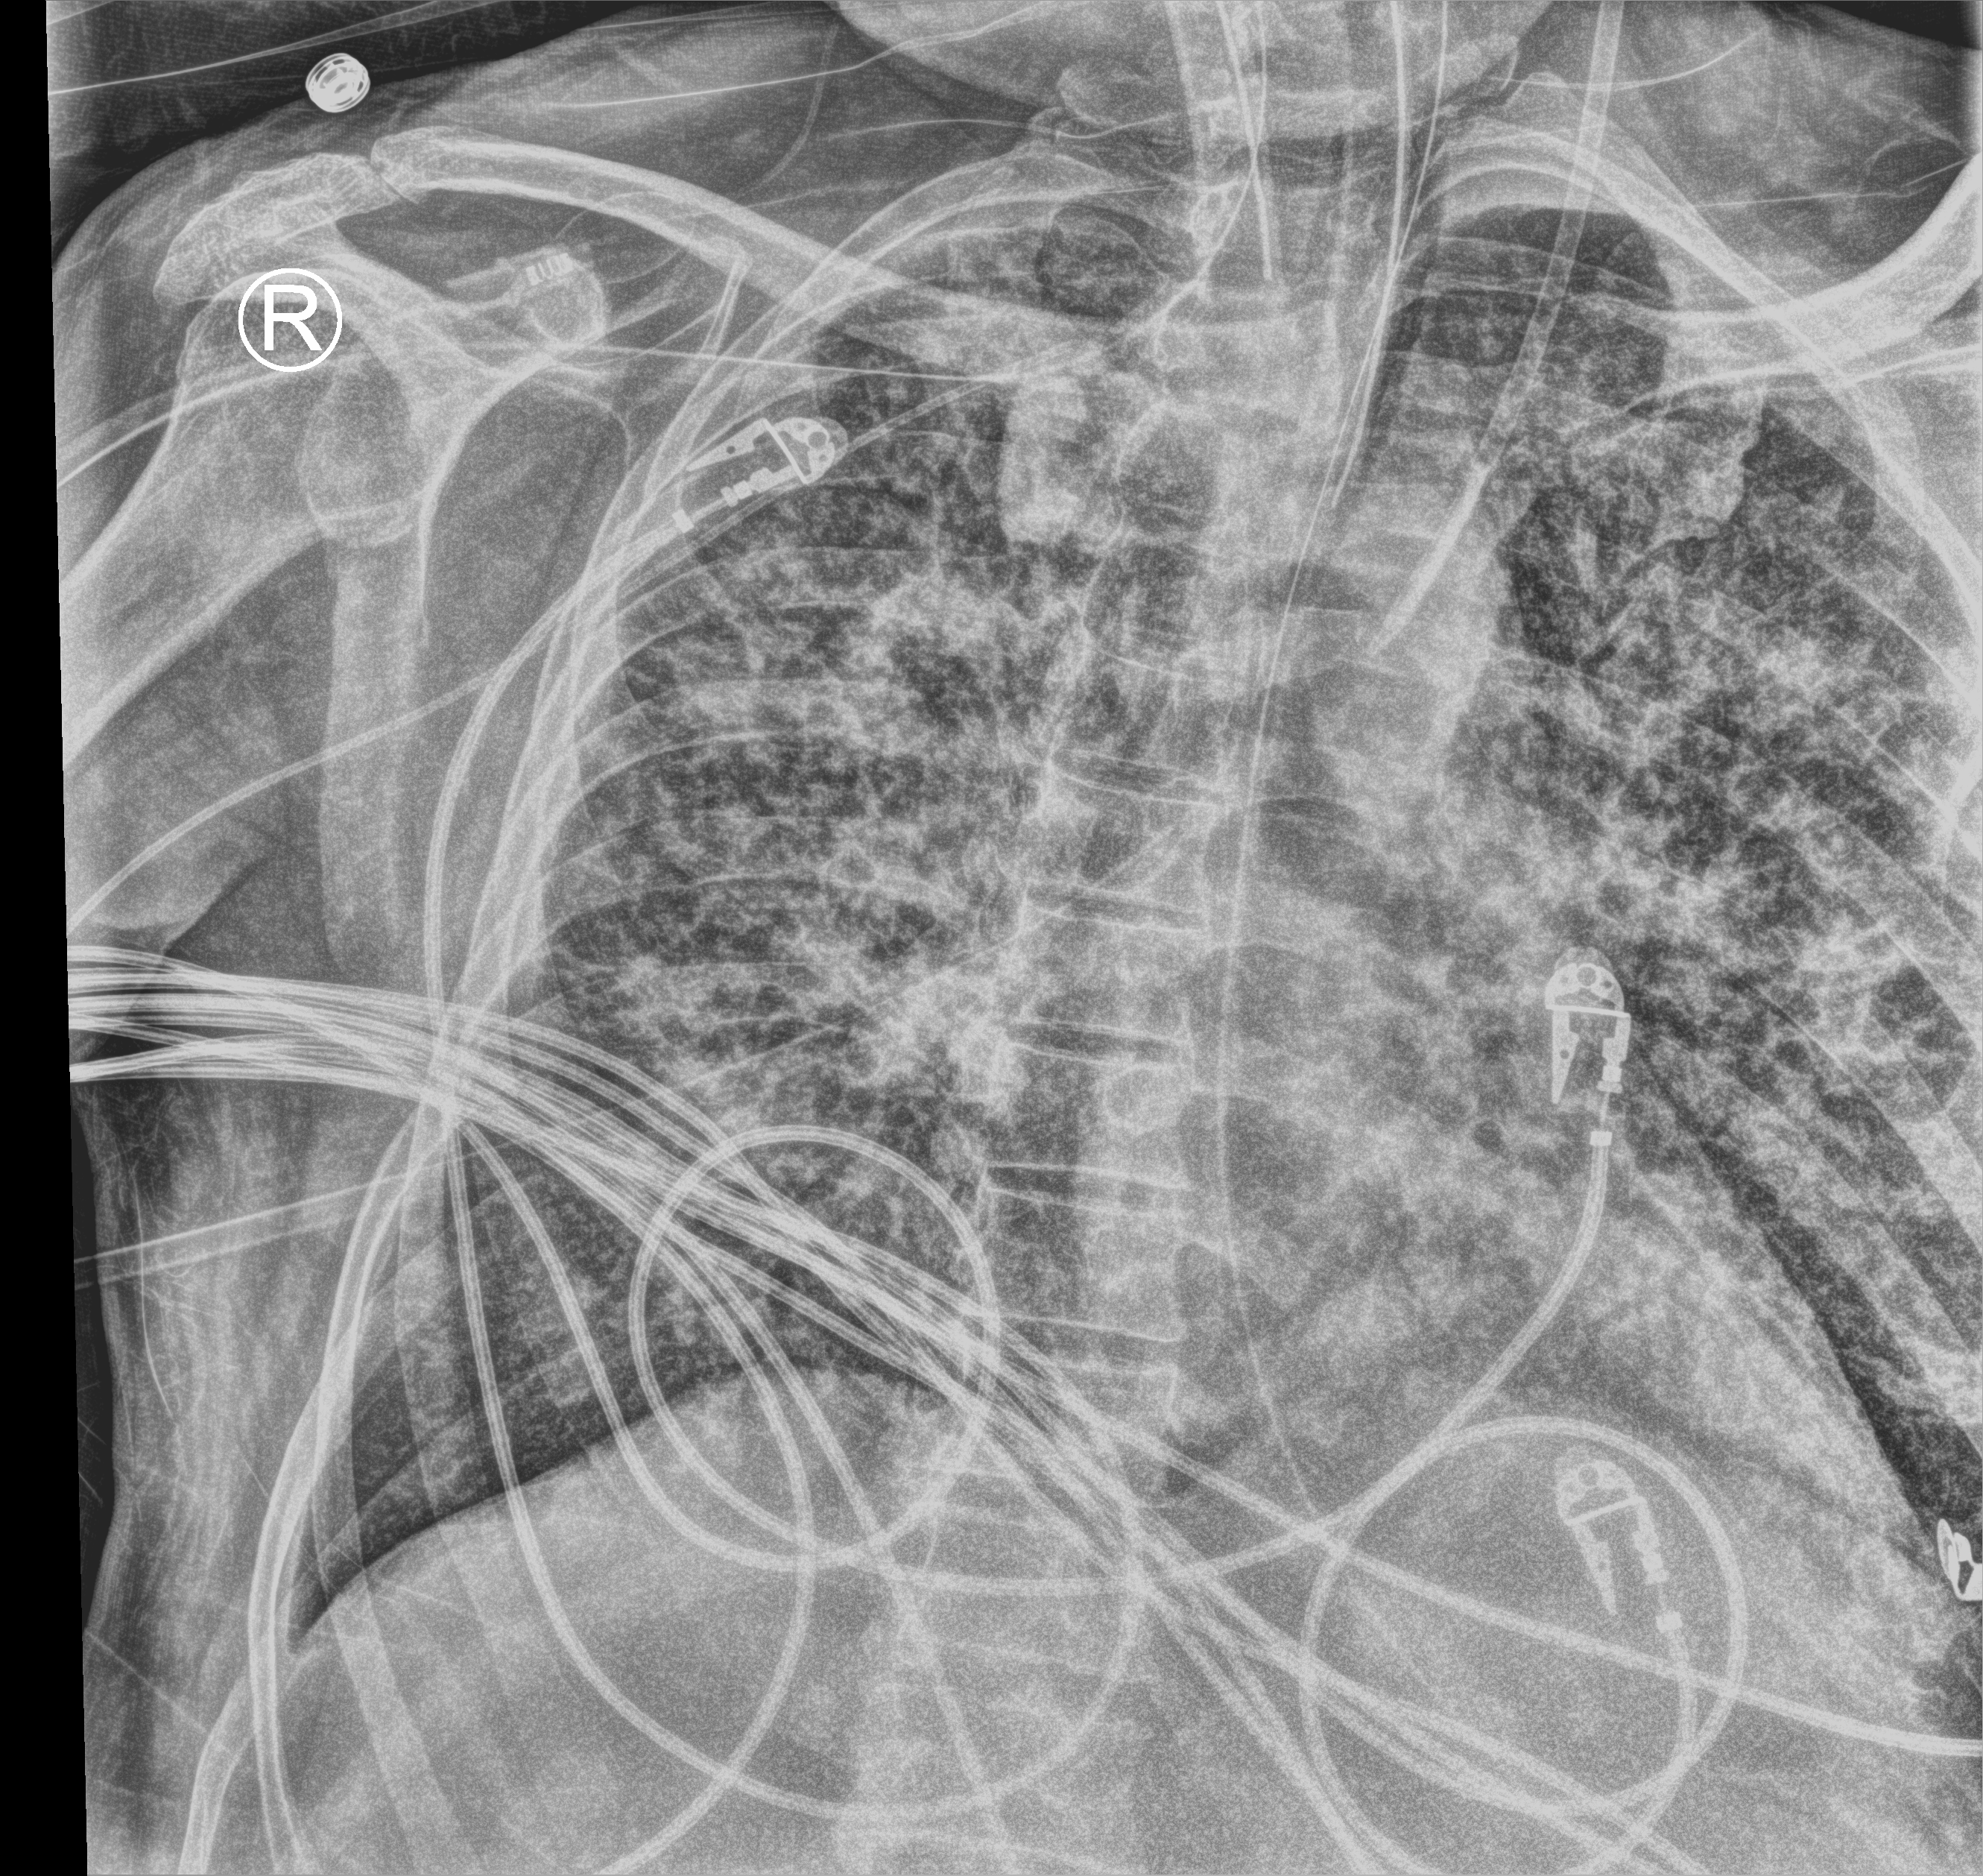
Portable chest radiograph; anteroposterior (AP) projection. Male patient hospitalised with COVID-19, age 60–74 years.
Hospital-stay facts (about this admission, not read from this image; timing relative to this image not recorded):
- admitted to intensive care during this hospital stay: yes
- mechanically ventilated during this hospital stay: yes
- length of hospital stay: 6 days